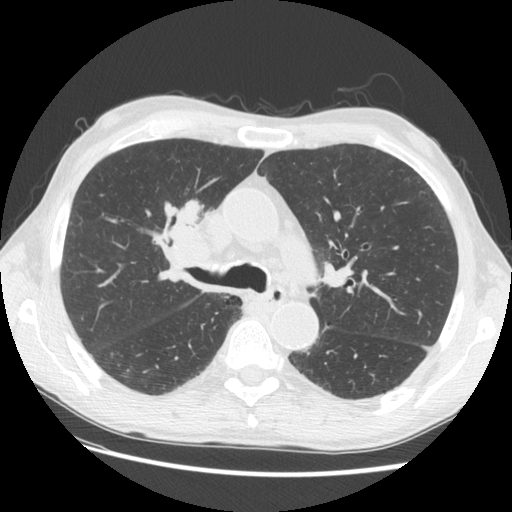
Low-dose screening chest CT, one axial slice. Slice 88 of 133 in the series (ordered by position). Lung window (W 1500 / L -600 HU). 2.5 mm slice thickness. 512 × 512 image matrix.
Annotated regions visible in this slice (expert manual segmentation):
- lesion 1 (tumor, hilum of right lung): bounding box (x1, y1, x2, y2) in pixels: (160, 198, 216, 261)